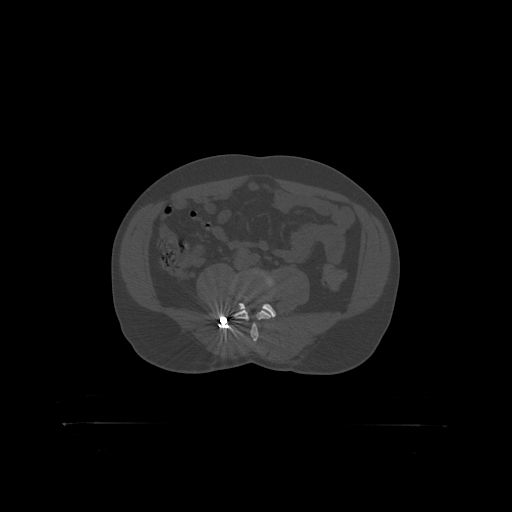
CT including the spine, one axial slice. Slice 222 of 399 in the series (ordered by position). Reconstruction kernel STANDARD. Bone window (W 1800 / L 400 HU). 512 × 512 image matrix, field of view 650 × 650 mm. Male patient, age 46 years. From the clinical record (not read from this slice): primary cancer: skin.
Annotated regions visible in this slice (semi-automatic segmentation, software-assisted and operator-edited):
- L4 vertebra: box from (x=235, y=271) to (x=277, y=319) px
- L5 vertebra: (x=238, y=297)–(x=276, y=316)